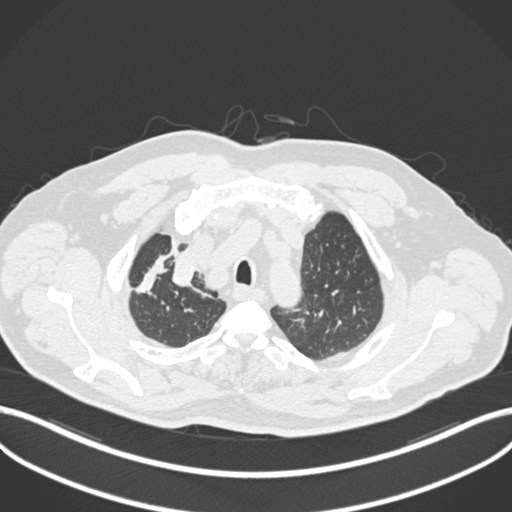
Chest CT, one axial slice; position 170 of 255 along the scan axis; 120 kVp; lung window (W 1500 / L -600 HU); 1 mm slice thickness; 512 × 512 image matrix, field of view 400 × 400 mm. Patient: male, 60 years. From the clinical record (not read from this slice): clinical TNM (as recorded): T1b N1 M0.
Annotated regions visible in this slice (bounding box drawn by a radiologist):
- lung tumour (recorded histology: squamous cell carcinoma): box from (x=165, y=246) to (x=198, y=292) px